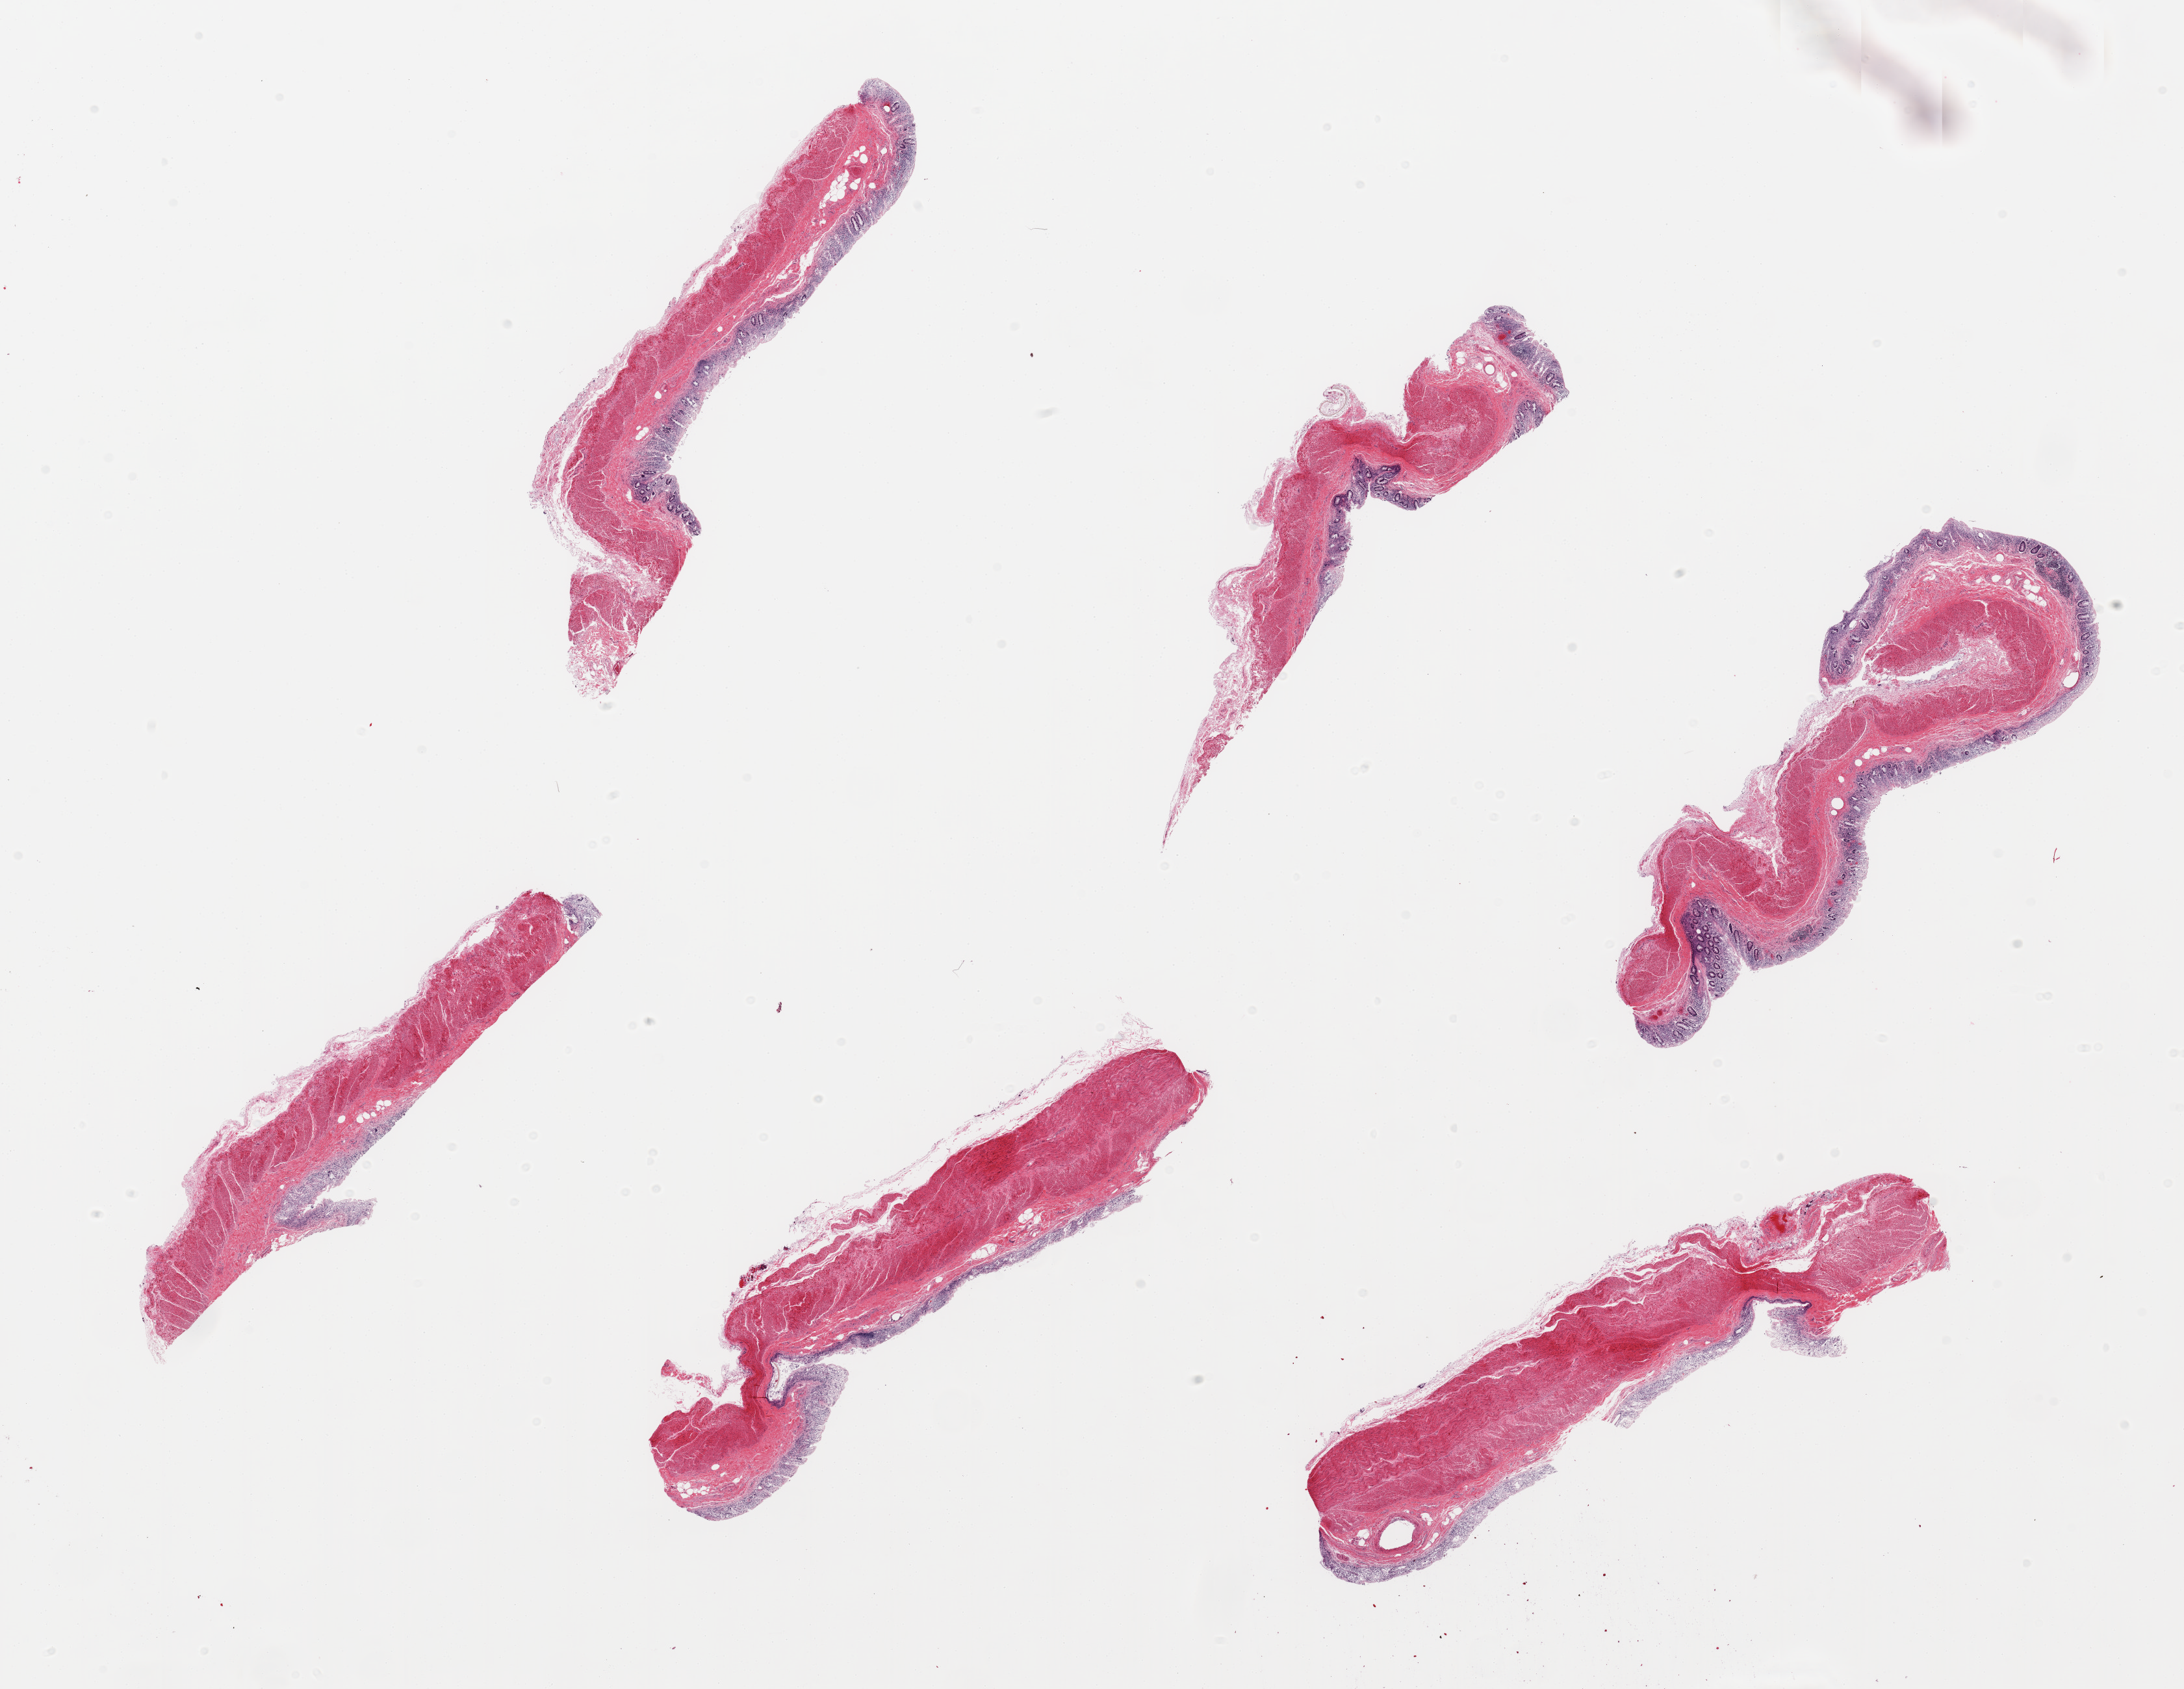
Digitized haematoxylin and eosin-stained section — low-resolution overview of the scanned area, about 26.6 x 20.6 mm (slide scanned at 20x); PAXgene-fixed, paraffin-embedded tissue; section of transverse colon (target tissue); tissue donor sample. Donor: male.
* review note (as recorded): 6 pieces; muscularis and moderately to severely autolyzed mucosa